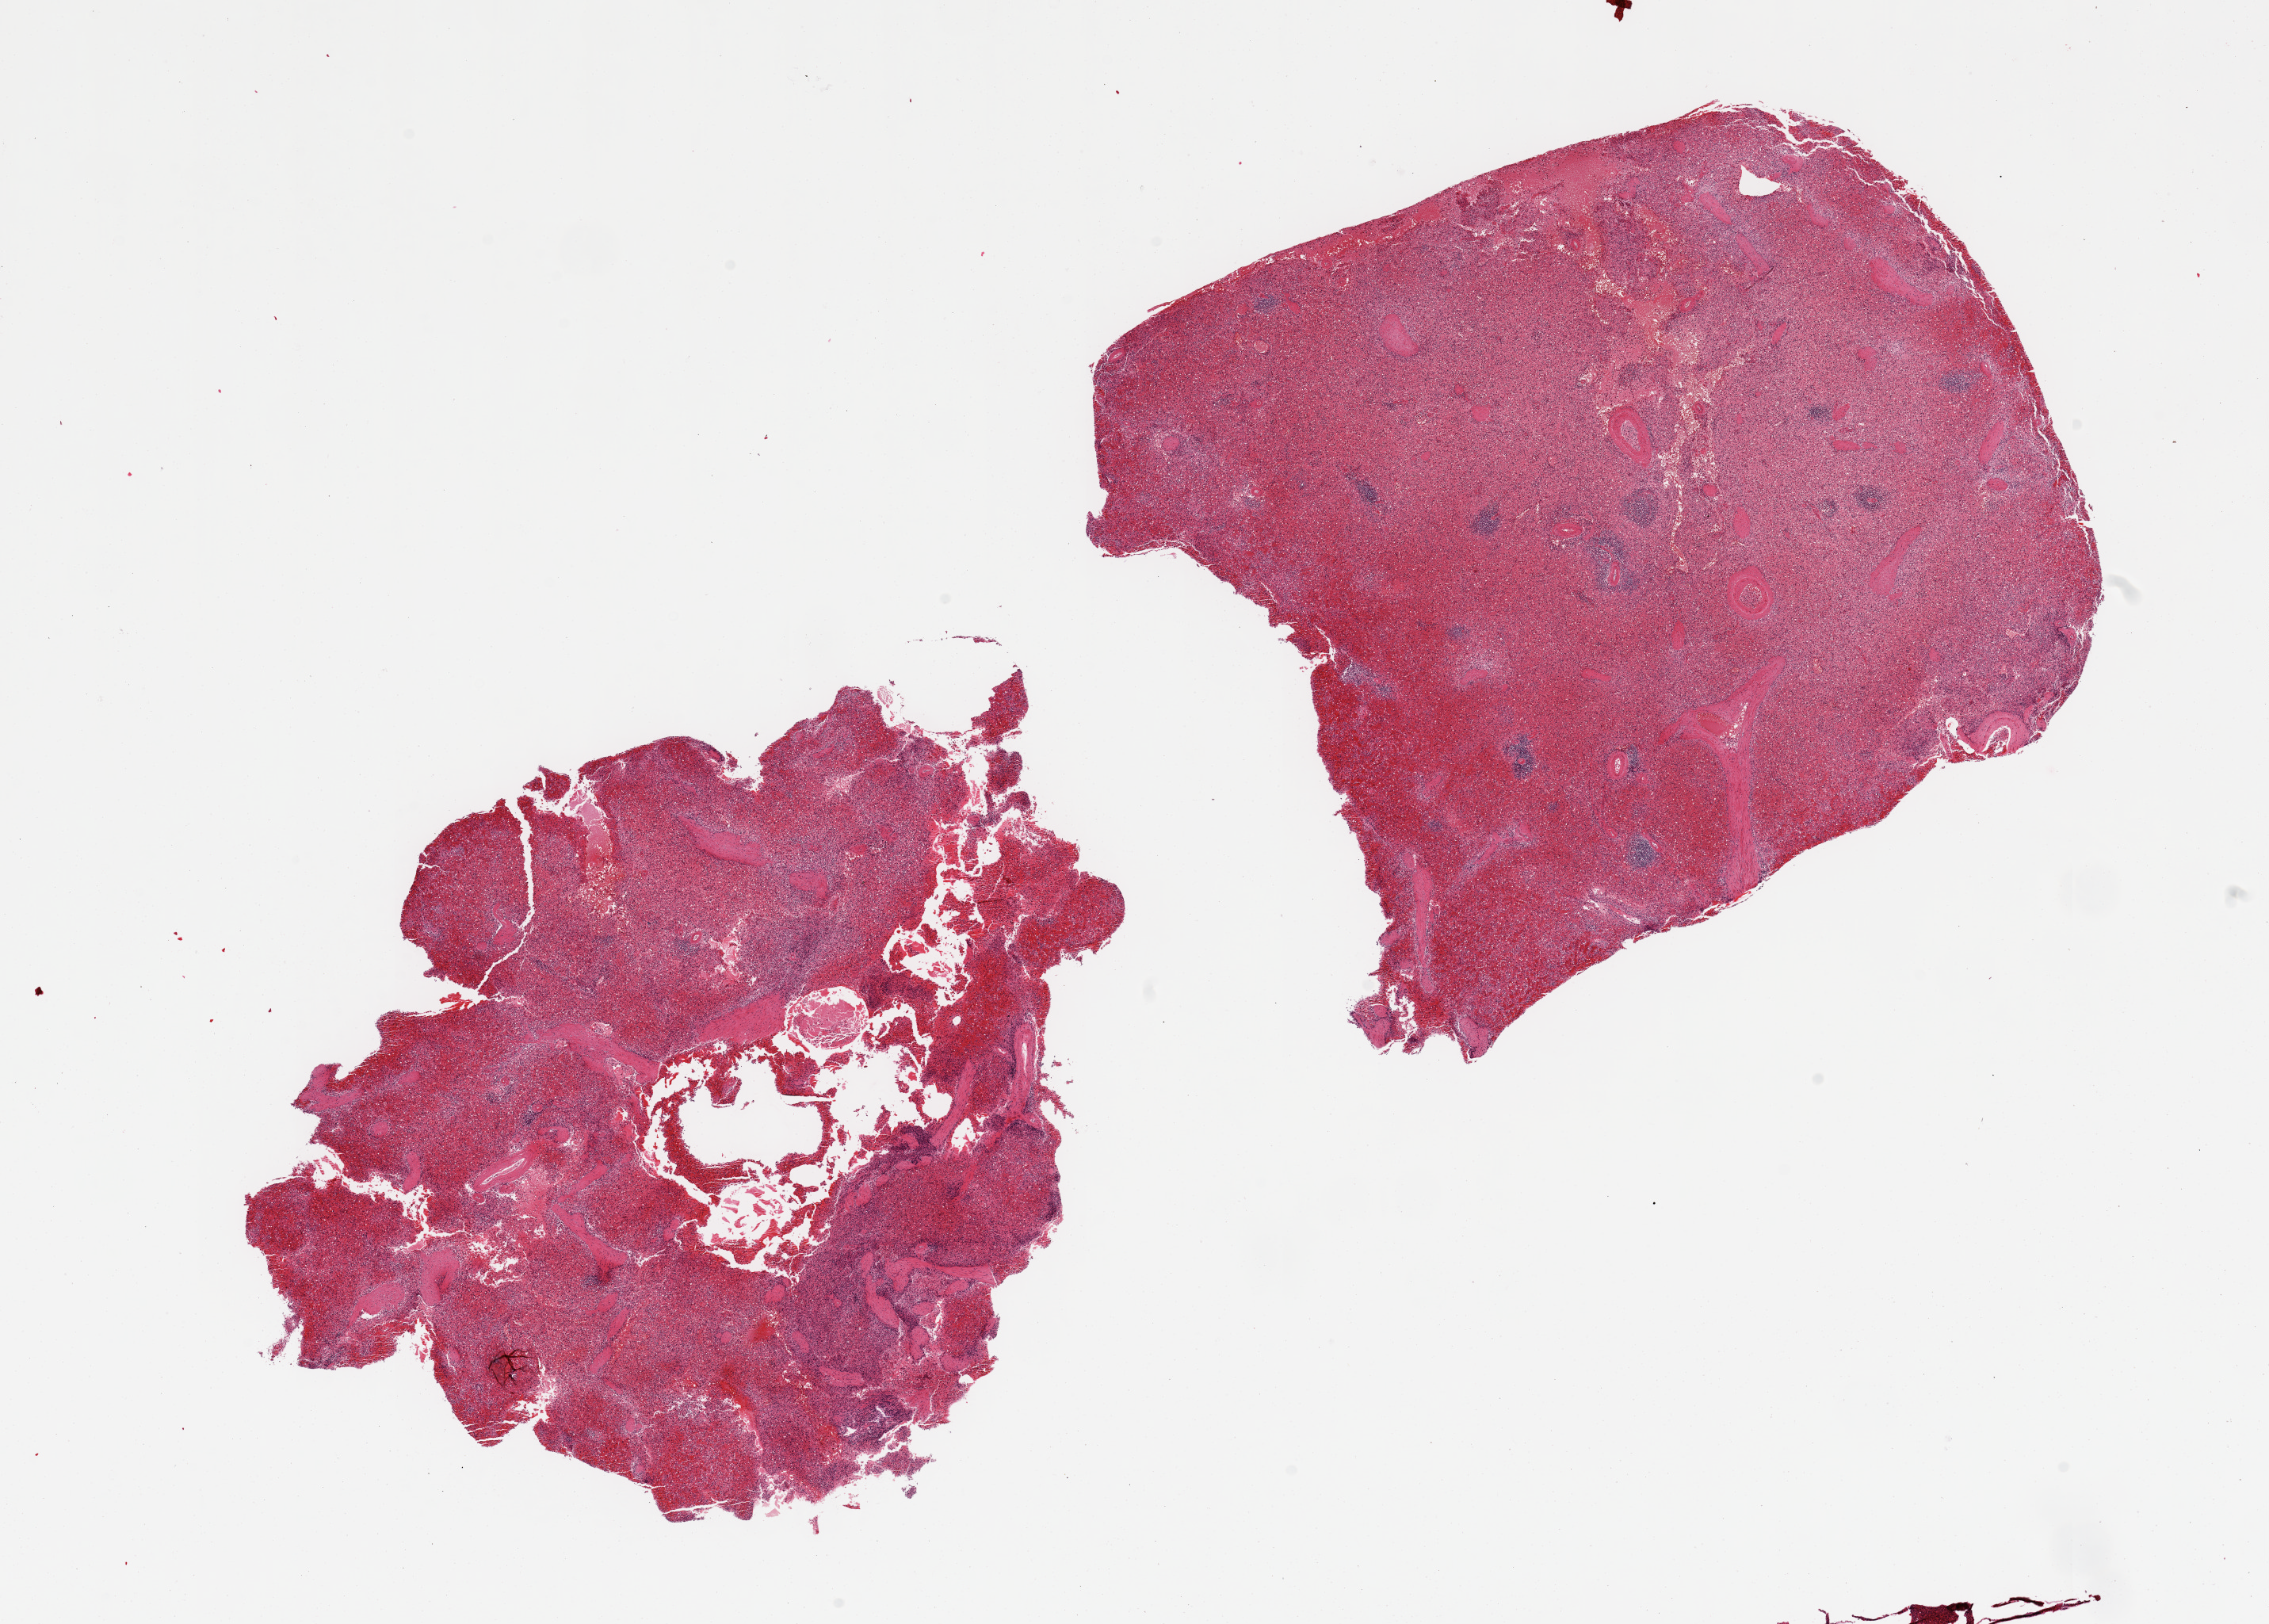
Hematoxylin and eosin (H&E) whole-slide image — whole scanned area (about 22.6 x 16.2 mm, acquisition: 20x scan) shown as a low-resolution overview. PAXgene-fixed, paraffin-embedded tissue. Target tissue: spleen. Tissue donor sample.
• reviewer comment on this tissue sample: 2 pieces, moderate congestion